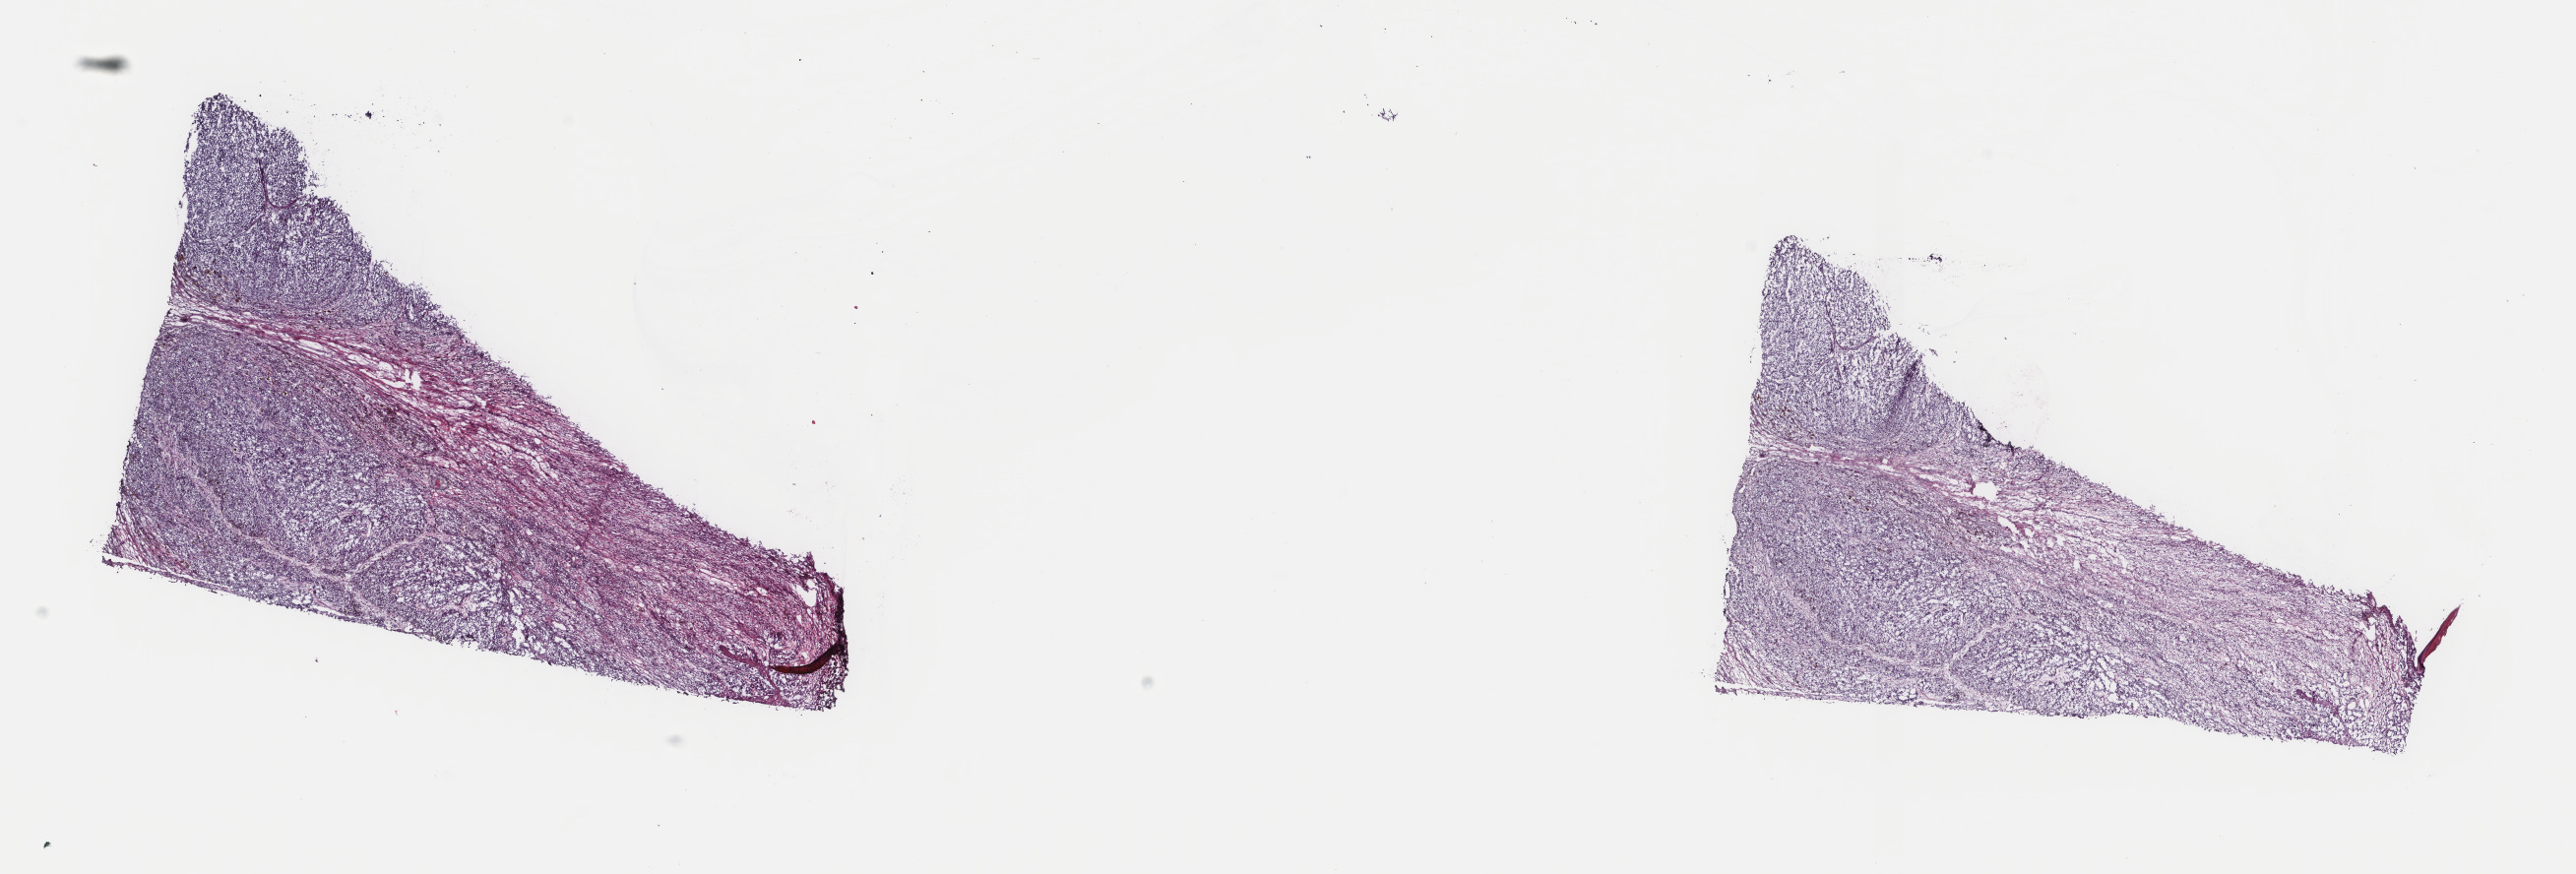
Hematoxylin and eosin (H&E) stained whole-slide image — whole scanned area (about 20.8 x 7.0 mm) shown as a low-resolution overview; frozen section from the top of the tissue portion; skin, primary tumour sample. Male, age 37 years at initial diagnosis. Pathologist review of this section (percent, as recorded): tumour cells 75%, tumour nuclei 75%, normal cells 0%, stromal cells 25%, necrosis 0%. Inflammatory infiltration, as recorded: lymphocyte infiltration 5%, monocyte infiltration 0%, neutrophil infiltration 0%.
- histologic diagnosis: Nodular melanoma
- TNM: T4b N0 M0
- AJCC pathologic stage: IIC (7th edition)